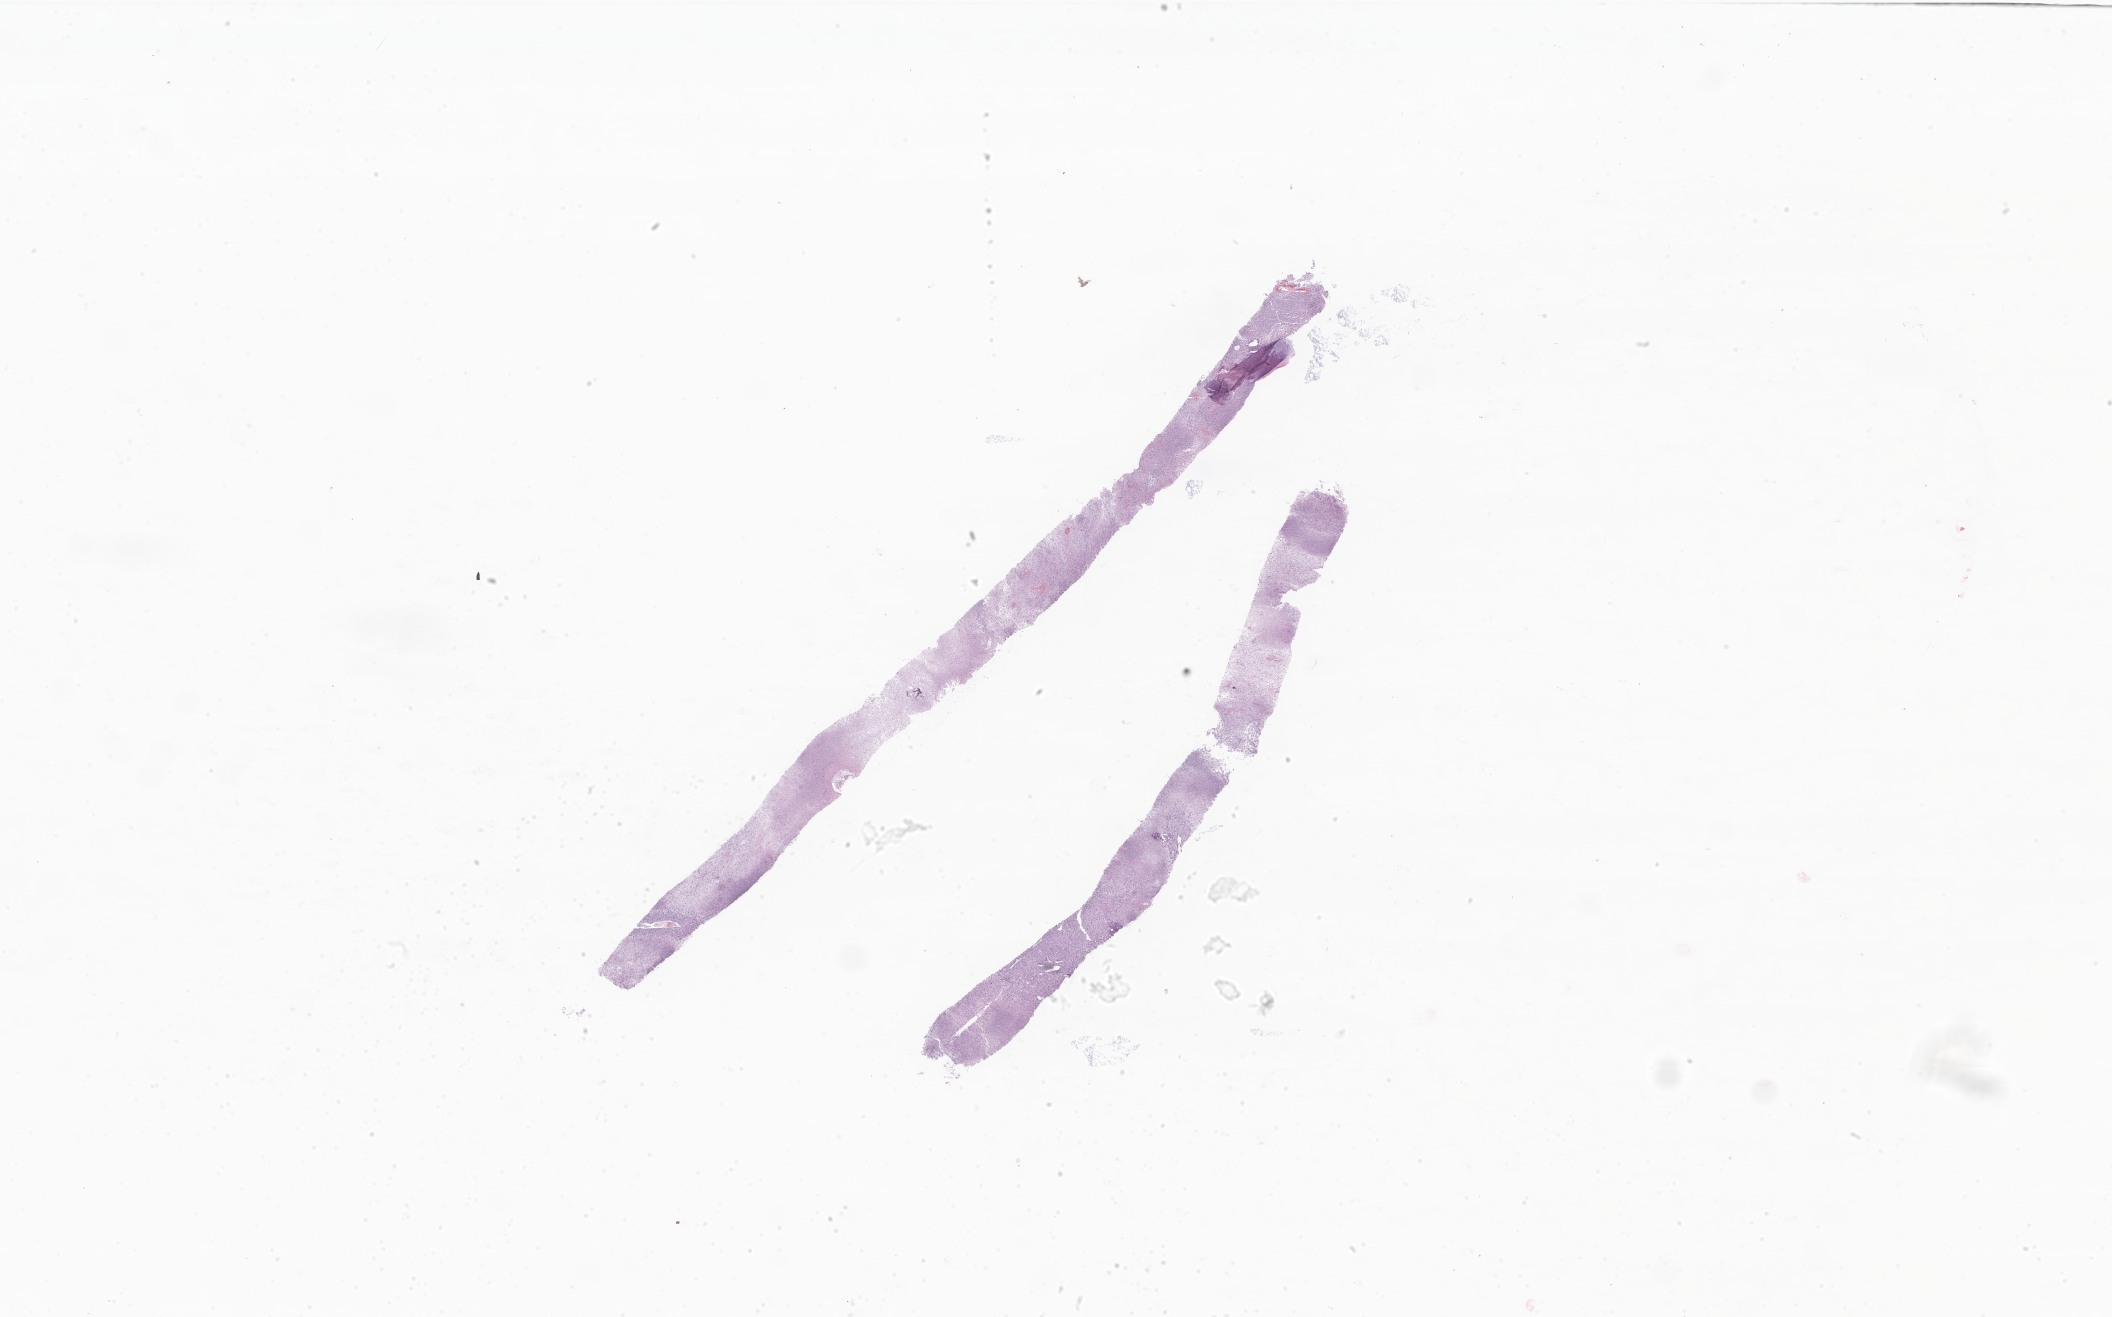
Digitized haematoxylin and eosin-stained section of tumor tissue from the short bone of upper limb, whole scanned area (about 35.6 x 22.2 mm) shown as a low-resolution overview, FFPE section. Patient male; age 248 months (20 years 8 months).
Diagnosis (ICD-O-3 morphology term): Pleomorphic rhabdomyosarcoma, adult type.